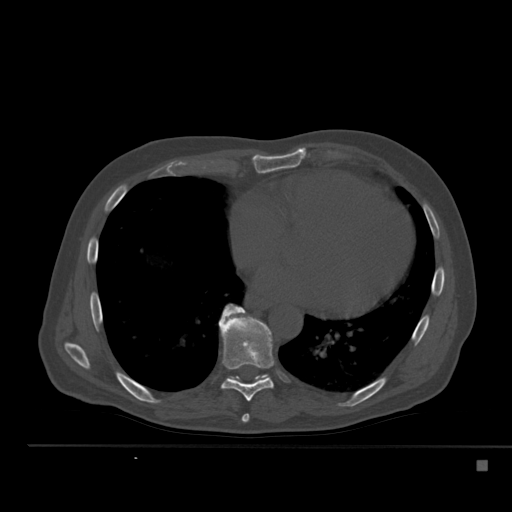
CT including the spine, one axial slice; position 305 of 517 along the scan axis; reconstruction kernel Br40s; 120 kVp; bone window (W 1800 / L 400 HU); 512 × 512 image matrix, field of view 408 × 408 mm. Patient: male, 70 years. Case-level facts recorded for this patient, not image findings: primary cancer: renal; vertebrae with lytic lesions (as recorded): T4, T6, T10, T12, L3, L4, L5.
Annotated regions visible in this slice (semi-automatic segmentation, software-assisted and operator-edited):
- T7 vertebra: bounding box (x1, y1, x2, y2) in pixels: (242, 414, 250, 423)
- T8 vertebra: (219, 304, 274, 401)
- T9 vertebra: (229, 375, 269, 383)